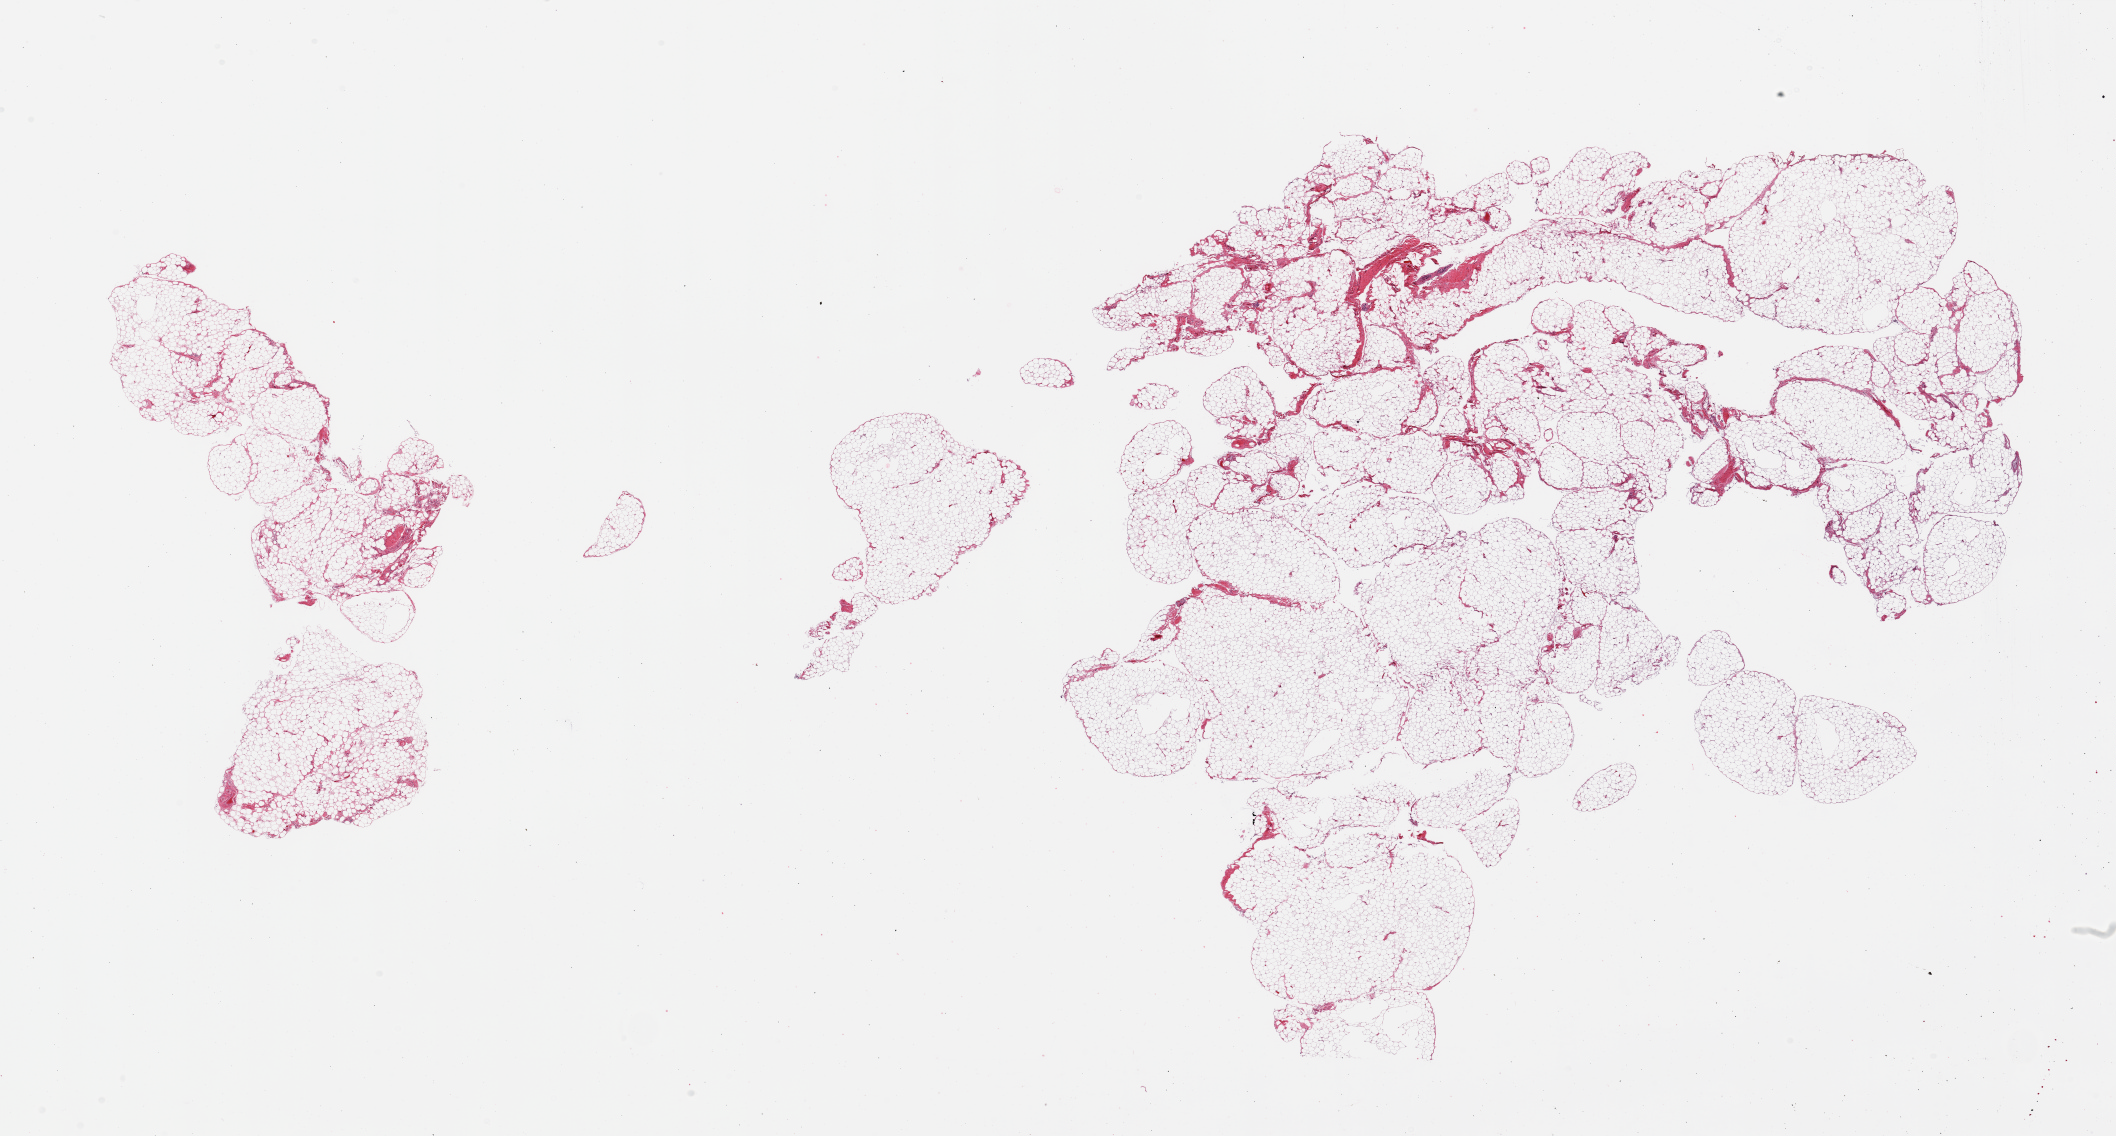
Digitized H&E-stained section, brightfield — whole scanned area (about 33.5 x 18.0 mm) shown as a low-resolution overview. PAXgene-fixed paraffin-embedded (PFPE) section. Sampled site (target tissue): omentum. Donor tissue sample.
Review note (as recorded): 2 pieces, ~5-10% fascia/vascular elements.